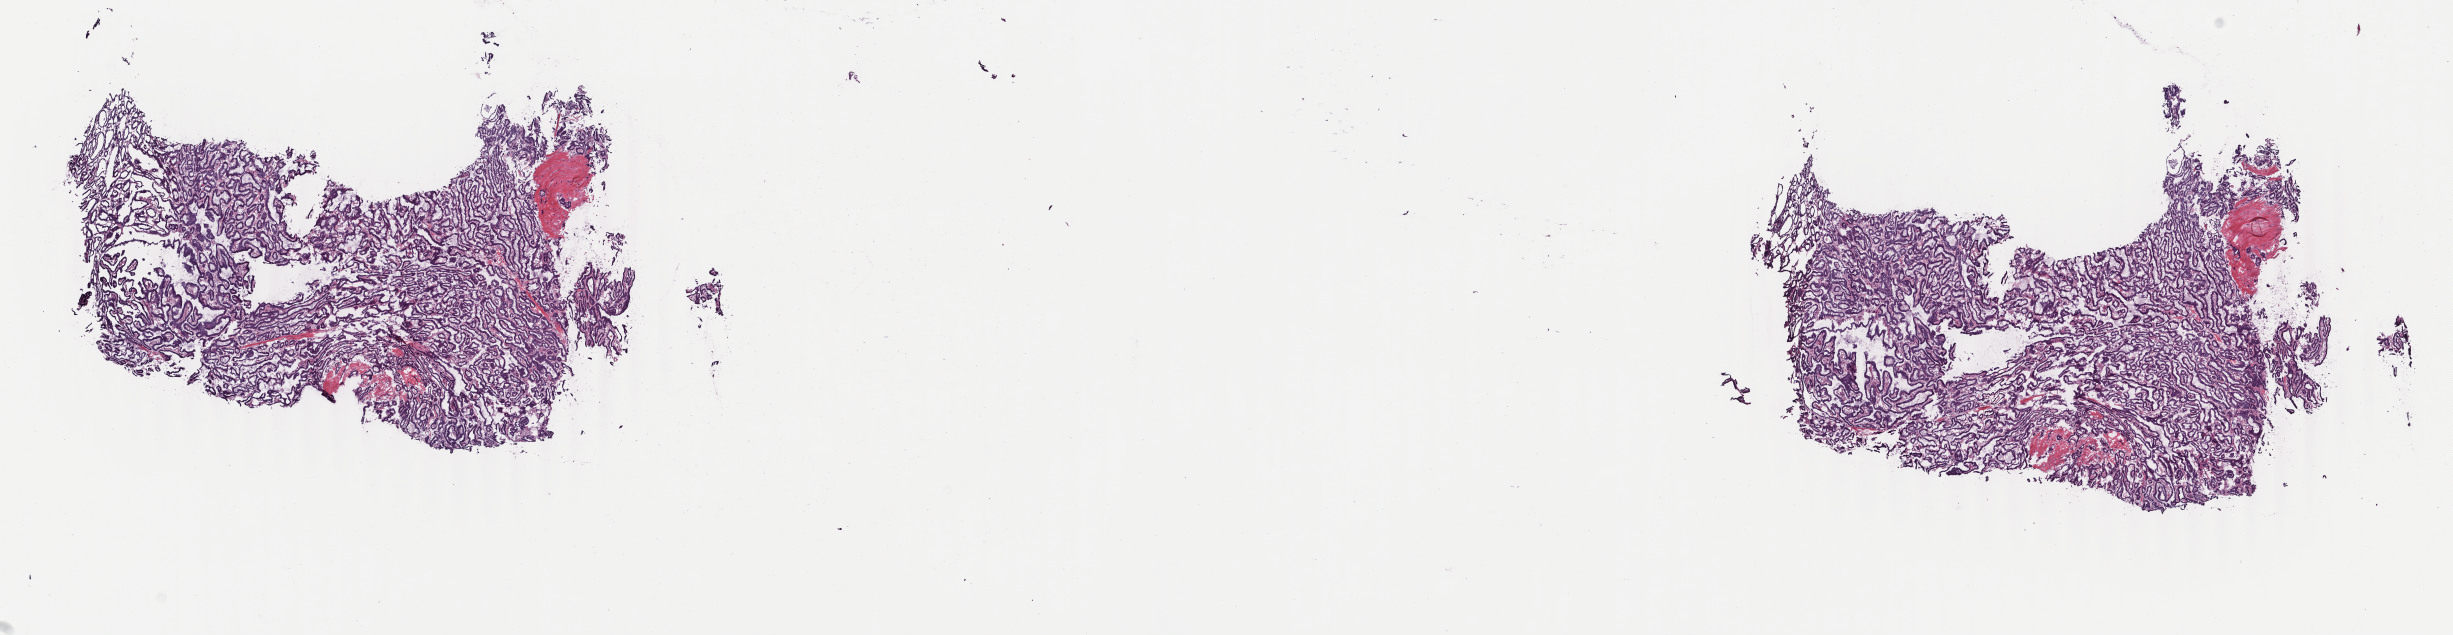
H&E whole-slide image — shown as a low-resolution overview of the whole scanned area (about 19.5 x 5.1 mm, slide scanned at 40x); frozen section; primary tumour sample from the thyroid. Female, age 20 years at initial diagnosis. Composition of this section per pathologist review: tumour cells 95%, tumour nuclei 80%, normal cells 0%, stromal cells 5%, necrosis 0%. Inflammatory infiltration, as recorded: lymphocyte infiltration 2%, monocyte infiltration 1%, neutrophil infiltration 0%.
* TNM: T2 N0 M0
* laterality: midline
* AJCC pathologic stage: I
* diagnosis: Papillary adenocarcinoma, NOS (thyroid gland)